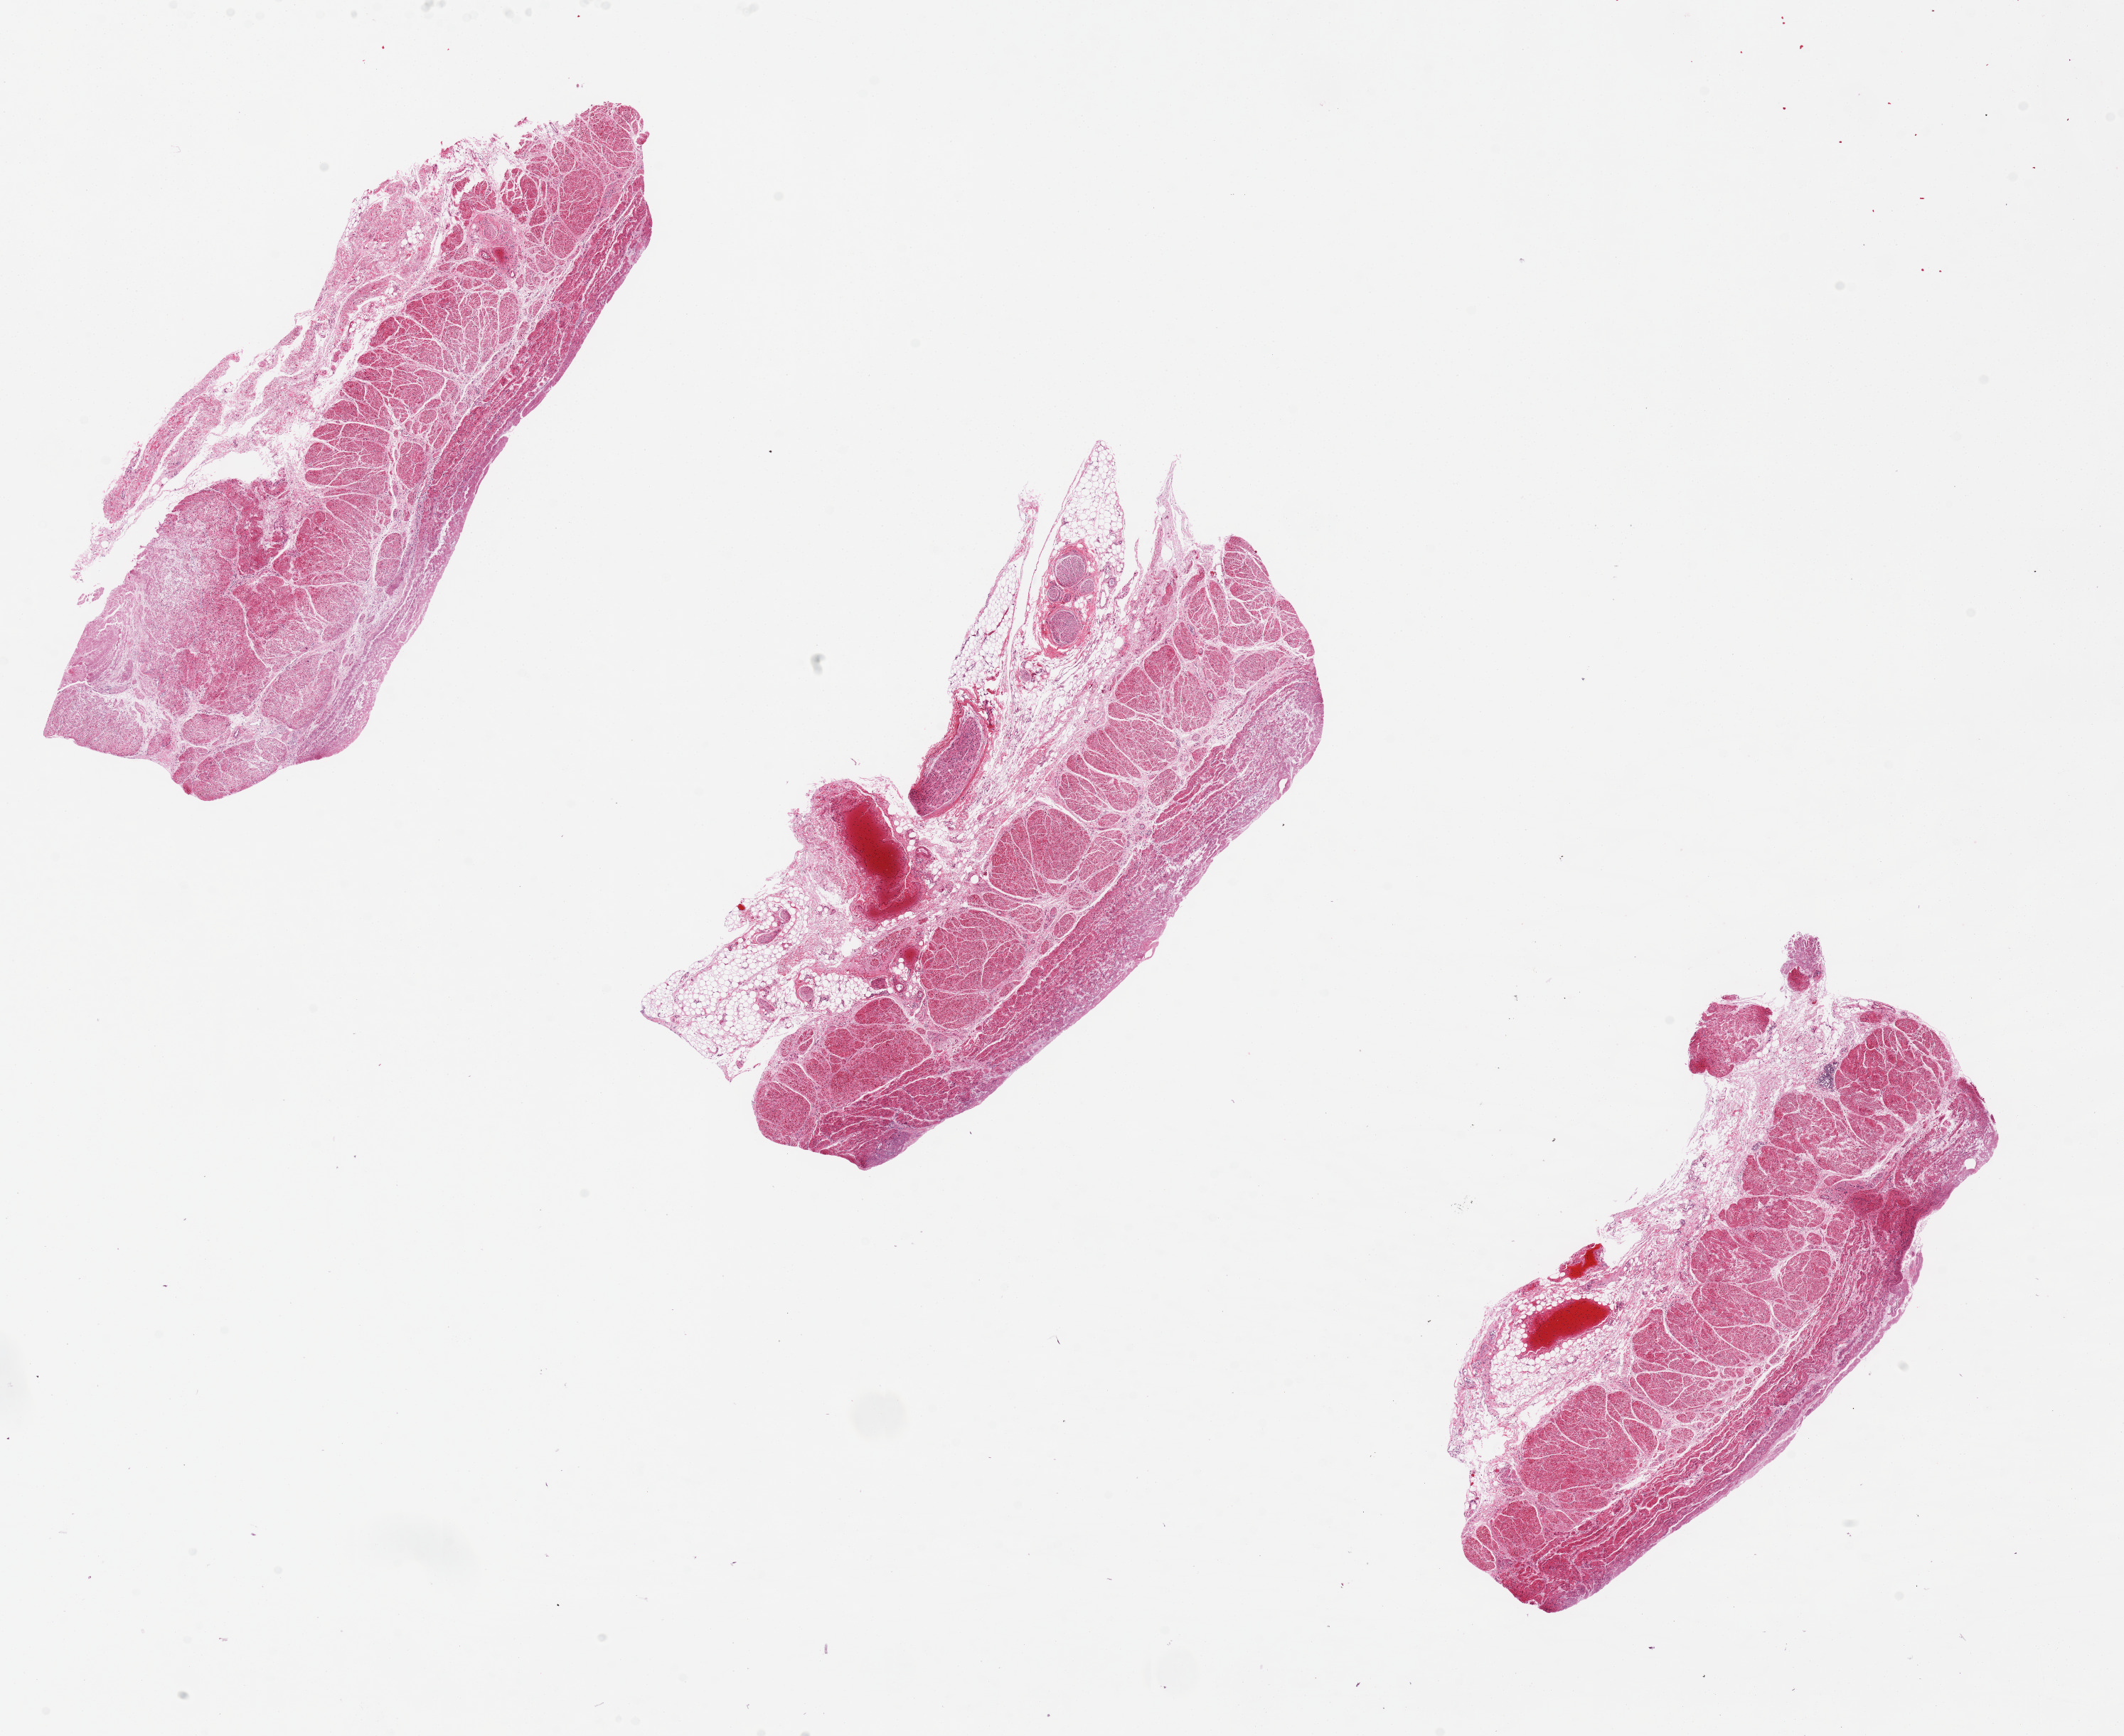
Haematoxylin and eosin whole-slide image, brightfield, whole scanned area (about 23.6 x 19.3 mm) shown as a low-resolution overview; PAXgene-fixed paraffin-embedded (PFPE) section; section of esophageal muscle (target tissue); tissue donor sample. Female donor.
Reviewer comment on this tissue sample: 3 pieces: 8.4x3.8mm. 1 with two large nerves.